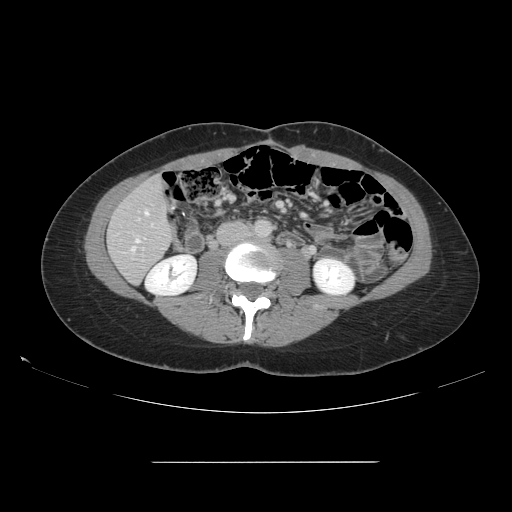
Contrast-enhanced abdominal CT, one axial slice; slice 40 of 151 in the series (ordered by position); 120 kVp; intravenous contrast given; soft-tissue window (W 400 / L 40 HU); 2.5 mm slice thickness; 512 × 512 image matrix. Female patient, age 46 years. Case-level facts recorded for this patient, not image findings: diagnosis: colorectal cancer liver metastases, imaged before liver resection; multiple liver metastases: yes; largest metastasis: 3 cm; chemotherapy before resection: no.
Outlined on this slice (outlined manually by an expert reader):
- hepatic veins: bounding box (x1, y1, x2, y2) in pixels: (132, 210, 149, 252)
- liver: (109, 177, 174, 283)
- planned liver remnant (the part of the liver to remain after resection): (109, 177, 174, 283)